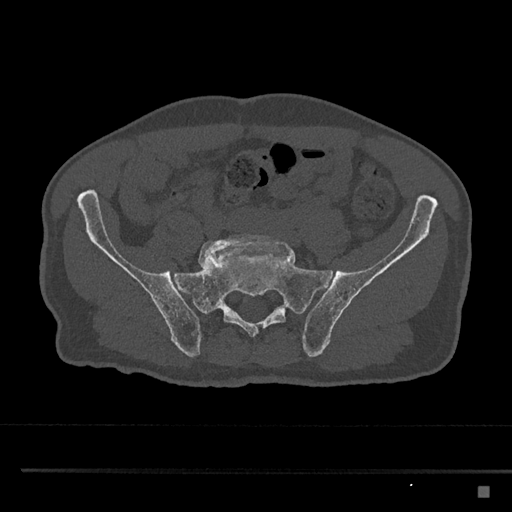
CT including the spine, one axial slice; position 533 of 797 along the scan axis; reconstruction kernel Br40s/3; 120 kVp; bone window (W 1800 / L 400 HU); 0.5 mm slice thickness; 512 × 512 image matrix. Patient: male, 59 years. From the clinical record (not read from this slice): primary cancer: prostate.
Structures marked on this image (semi-automatically segmented with operator editing):
- L5 vertebra: bounding box (x1, y1, x2, y2) in pixels: (198, 234, 288, 268)